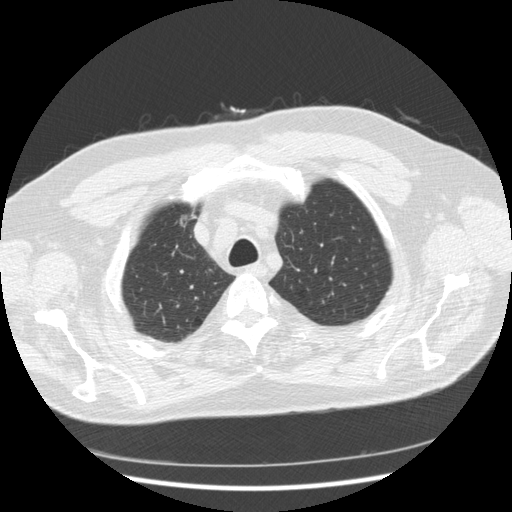
Axial slice from a low-dose chest CT screening exam, second annual screen, lung window (W 1500 / L -600 HU), standard (soft-tissue) reconstruction kernel (STANDARD). Male participant, aged 66 years at enrolment.
- Lesion marked by an expert reader, bounding box [x1, y1, x2, y2] px = [156, 203, 206, 242].
- No non-calcified nodule or mass ≥4 mm was recorded by the screening reader at this exam.
- Lung cancer was diagnosed 603 days after this screen (after the third annual screen): bronchiolo-alveolar adenocarcinoma, NOS, right upper lobe, moderately differentiated (G2), stage IA (AJCC 6th edition), 12 mm at pathology.